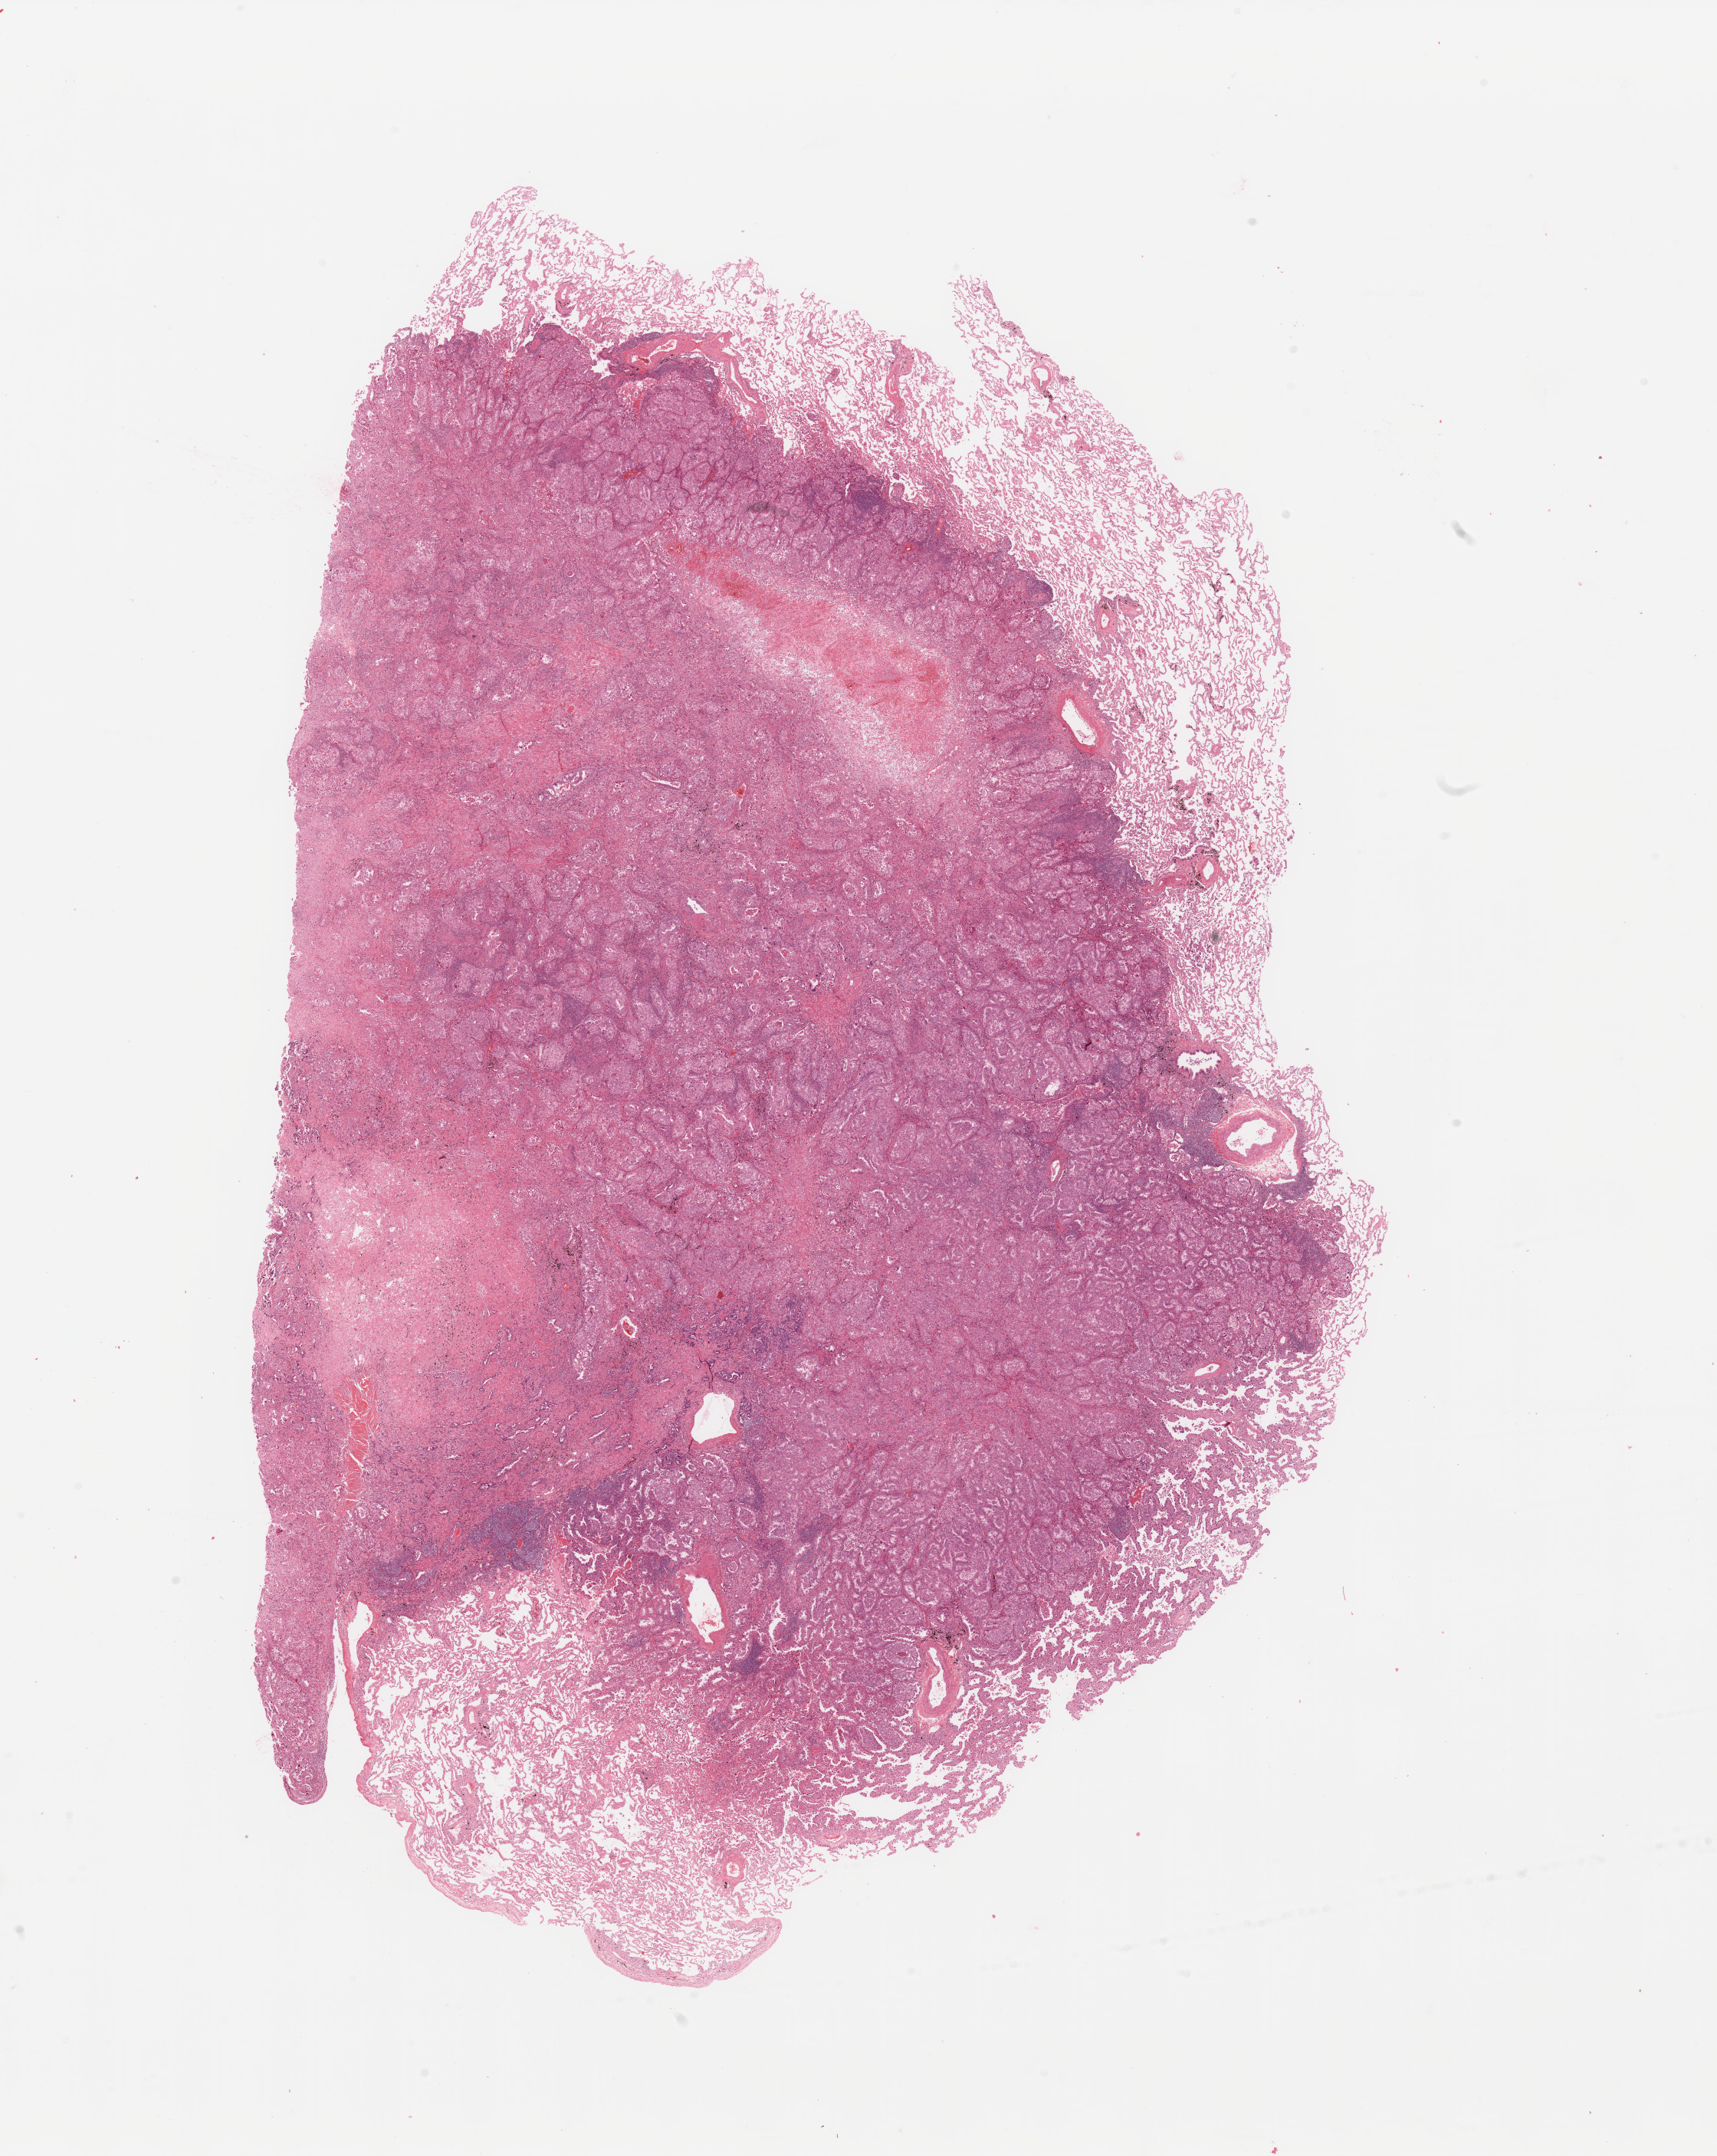
Whole-slide histology image, H&E-stained, whole scanned area (about 17.7 x 22.3 mm) shown as a low-resolution overview; tumour tissue sample, sampled site: lung. Female, 62 y/o. Histologic grade: G3 (poorly differentiated). Pathologist review of this section (percent, as recorded): tumour nuclei 70%, necrosis 5%.
AJCC pathologic stage: IB. Diagnosis: Adenocarcinoma, NOS. Primary tumour site (as recorded): left upper lobe.